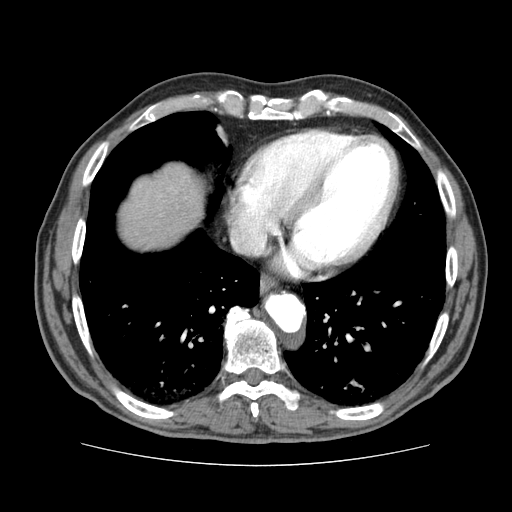
Contrast-enhanced abdominal CT (liver protocol), one axial slice; reconstruction kernel STANDARD; 120 kVp; soft-tissue window (W 400 / L 40 HU); 2.5 mm slice thickness; 512 × 512 image matrix, field of view 360 × 360 mm. Case-level facts recorded for this patient, not image findings: diagnosis: hepatocellular carcinoma (patient treated with transarterial chemoembolisation; whether this scan precedes or follows treatment is not stated here); TNM stage (as recorded): Stage-I; Child-Pugh class: A; tumour nodularity: uninodular.
Structures marked on this image (semi-automatic segmentation, software-assisted and operator-edited):
- abdominal aorta: bounding box (x1, y1, x2, y2) in pixels: (266, 294, 304, 331)
- liver parenchyma outside the tumour (the mass and vessels are separate outlines, so this box may not span the whole liver): (120, 164, 202, 248)